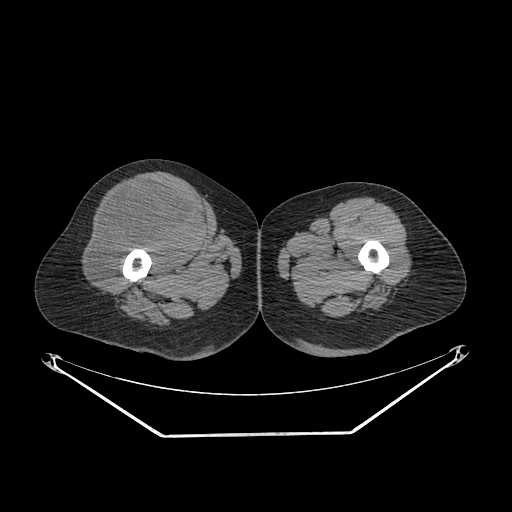
CT of an extremity soft-tissue mass (from a PET/CT study), one axial slice; position 257 of 311 along the scan axis; reconstruction kernel SOFT; soft-tissue window (W 400 / L 40 HU); 3.75 mm slice thickness; 512 × 512 image matrix. Female patient. From the clinical record (not read from this slice): histological type: pleiomorphic undifferentiated sarcoma; grade: high; site of the primary tumour: right quadricep.
Annotated regions visible in this slice (expert contour drawn on MRI and transferred to this co-registered scan by the dataset authors):
- tumour plus oedema (research contour): bounding box <91,183,199,287> (left, top, right, bottom; pixels)
- tumour (research contour): <91,183,199,287>